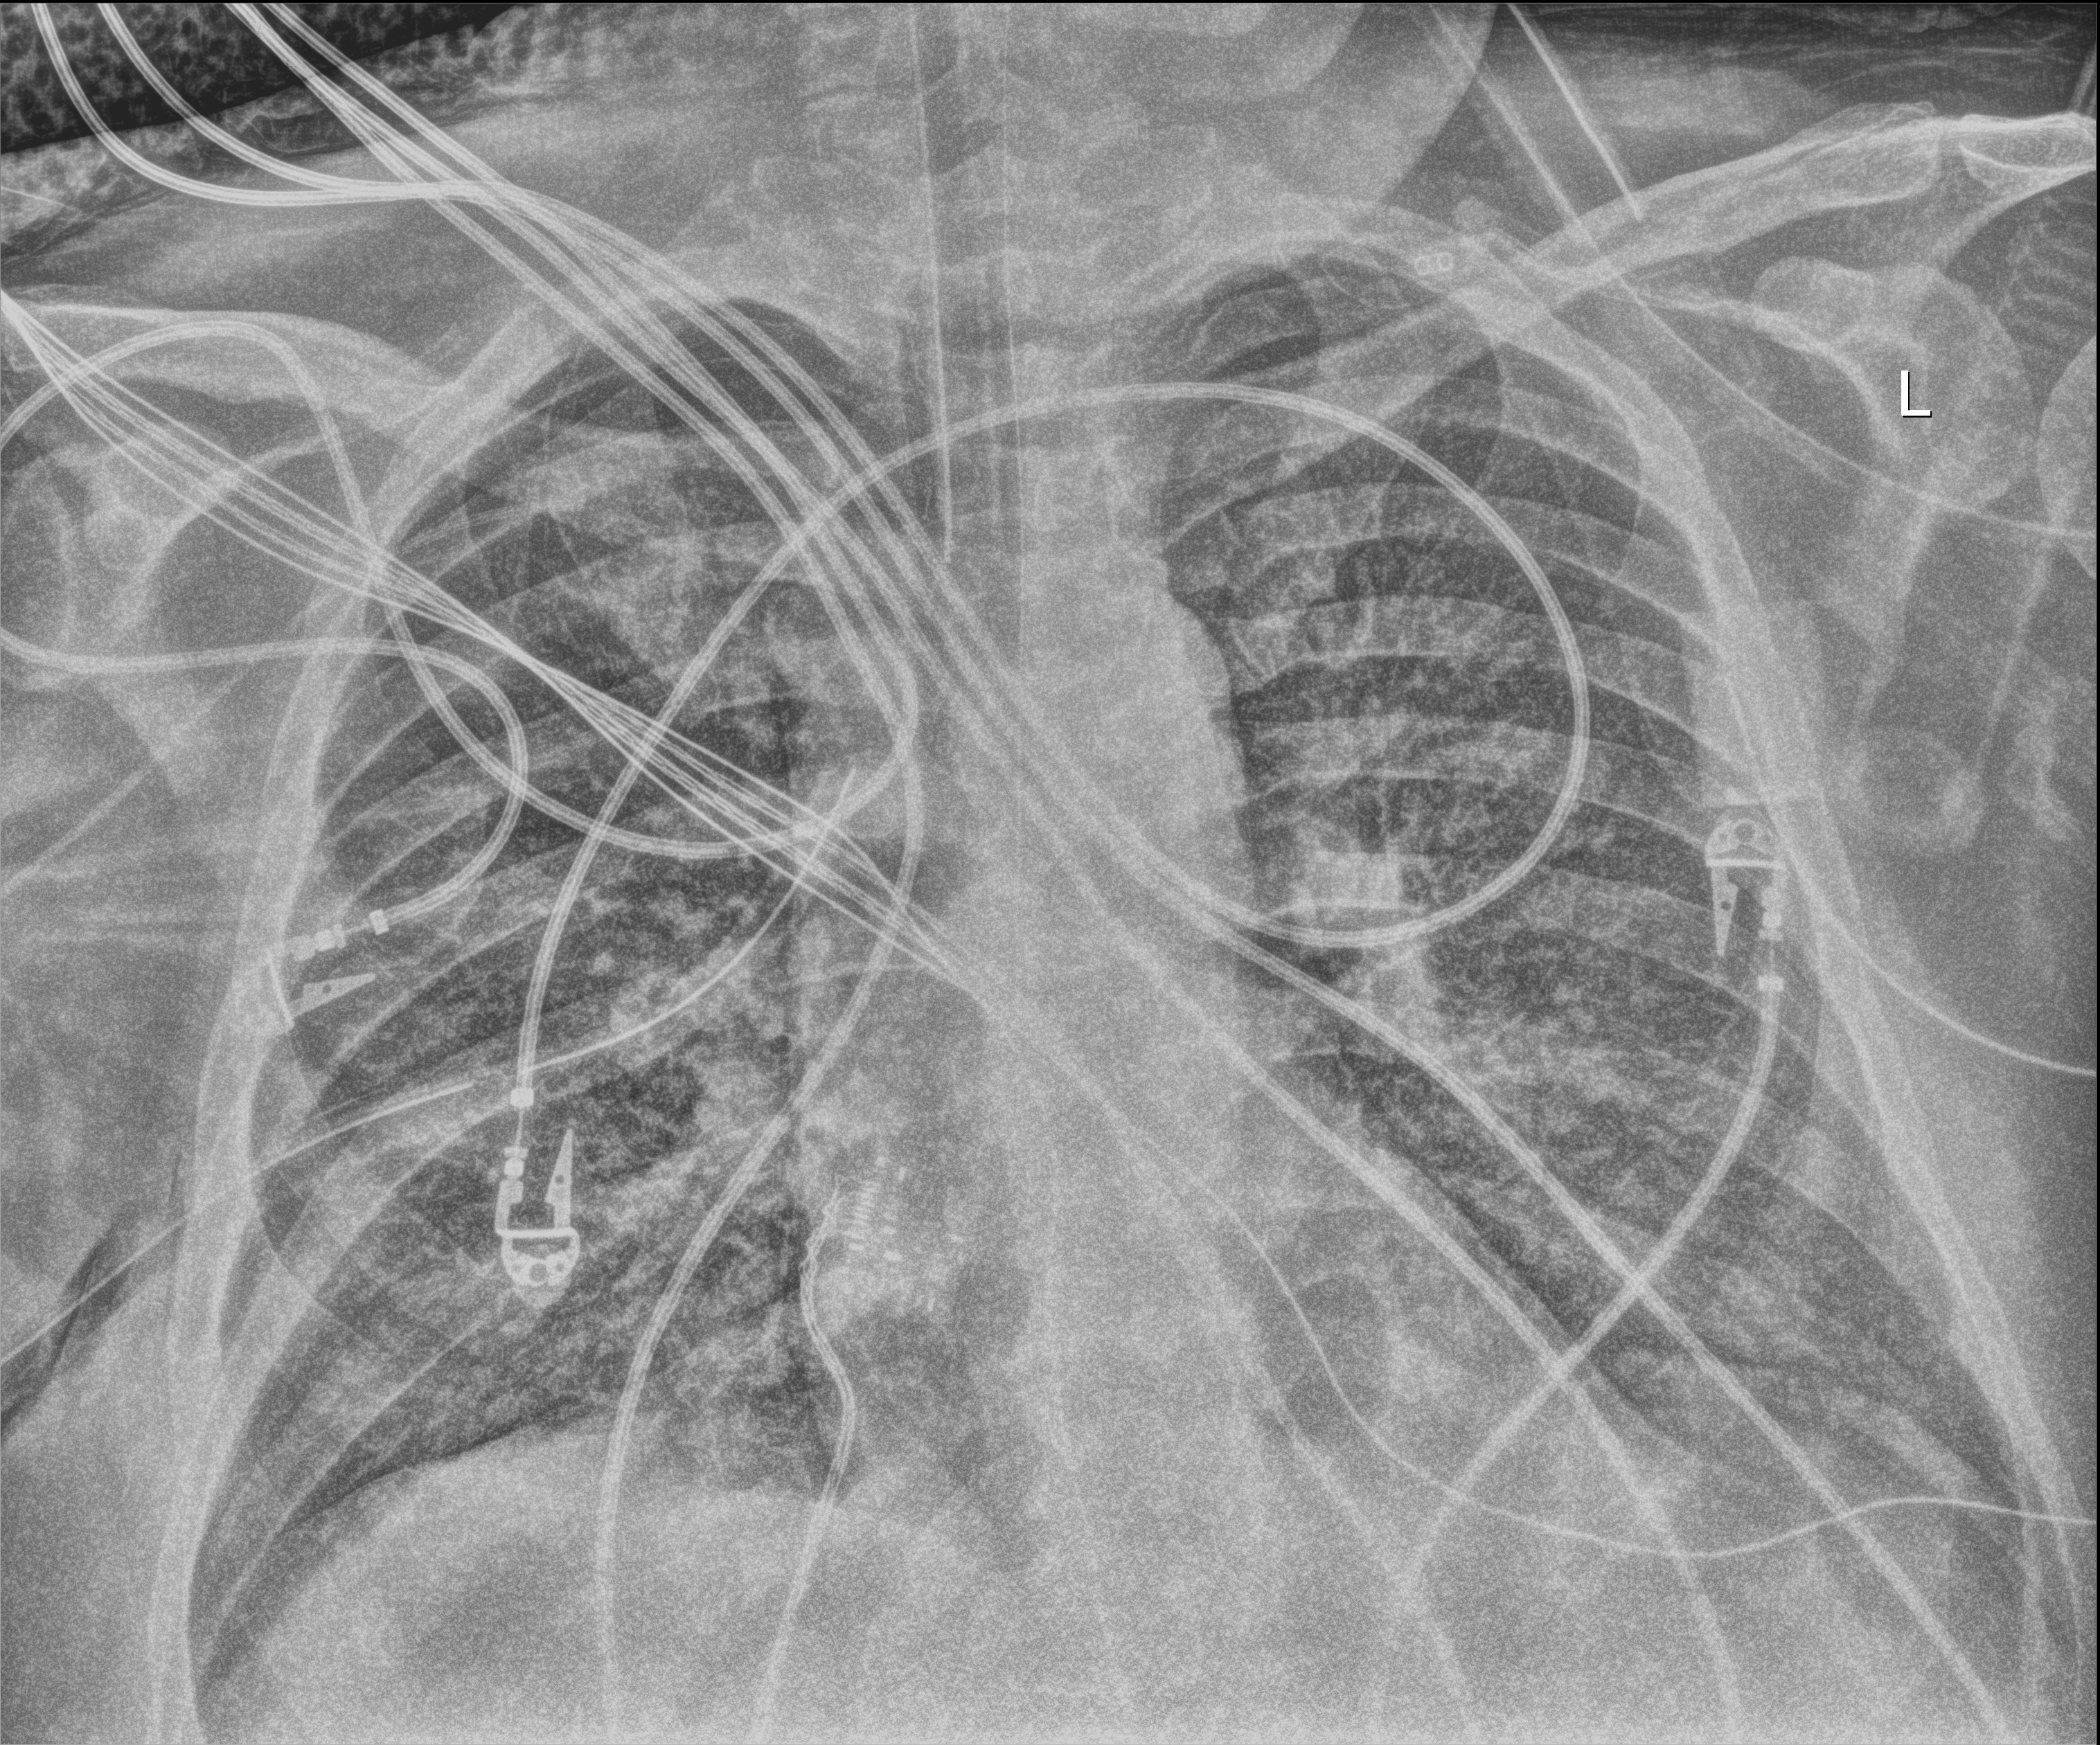
Chest X-ray (portable); anteroposterior (AP) projection. Adult patient hospitalised with COVID-19, age 18–59 years.
Admission-level facts for this patient (not findings on this image; timing relative to this image not recorded):
- mechanically ventilated during this hospital stay: yes
- admitted to intensive care during this hospital stay: yes